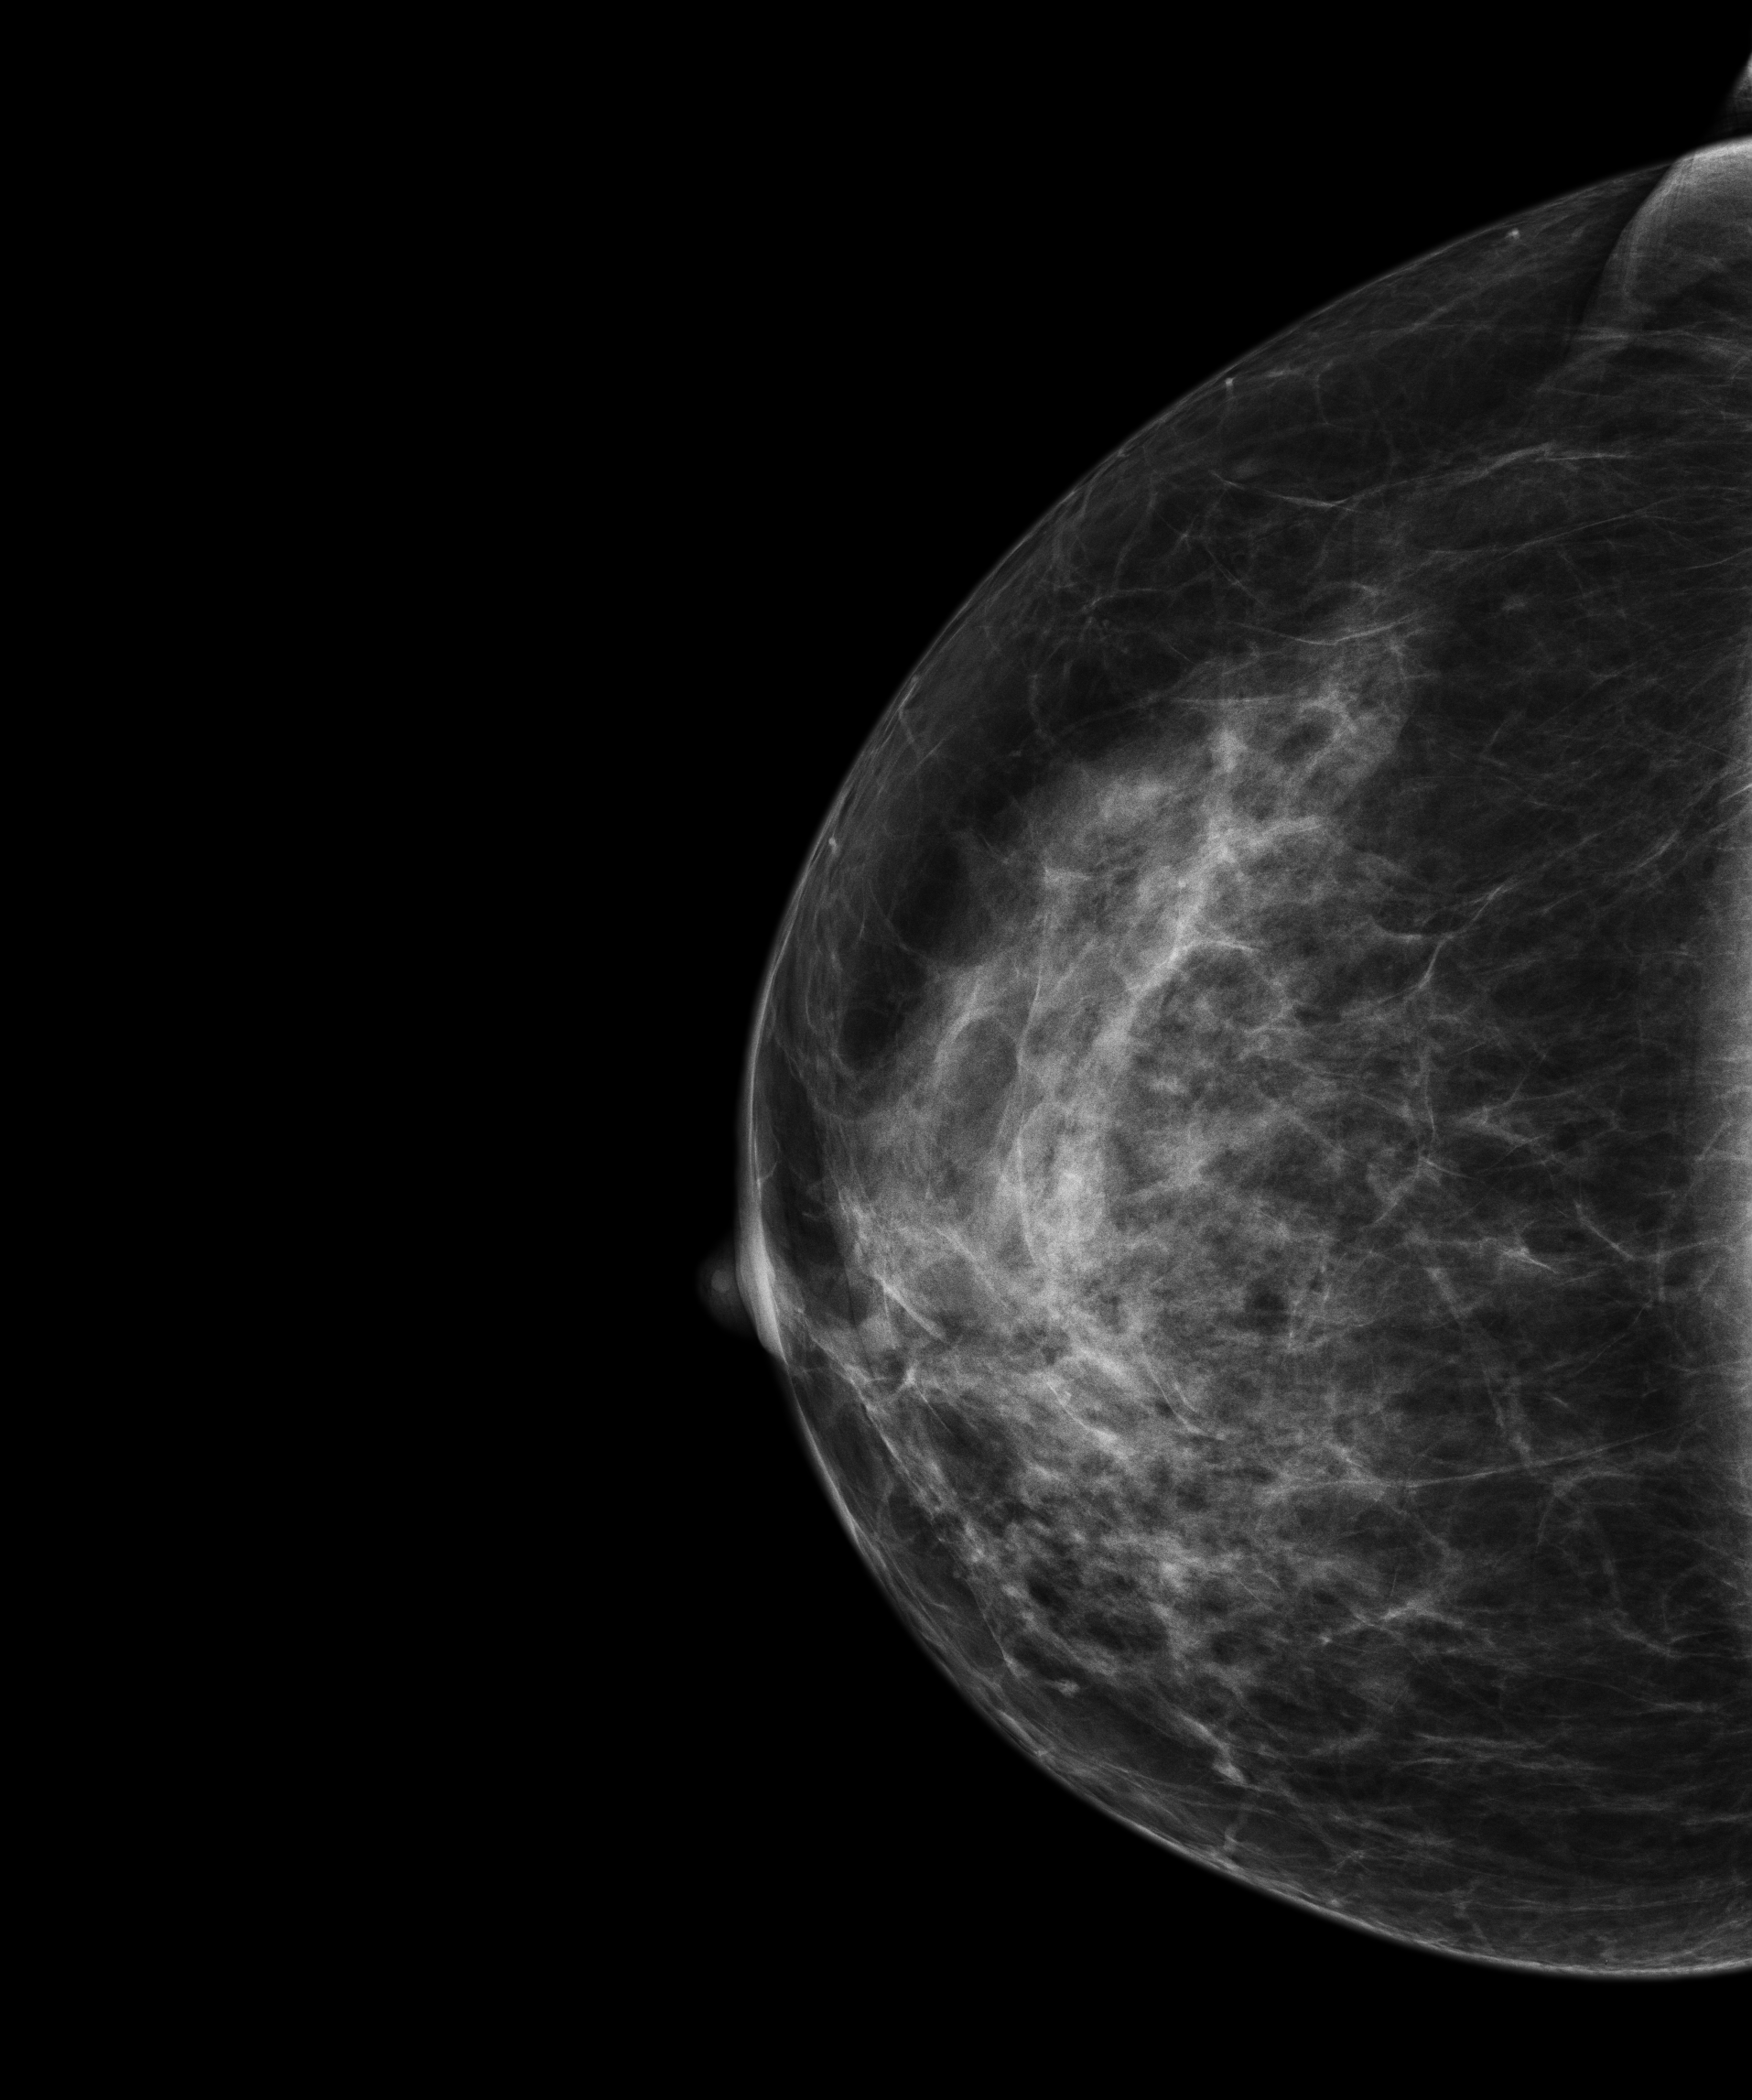
Digital mammogram (FFDM); right breast; cranio-caudal projection; annual screening mammography examination; compressed breast thickness 41 mm. Female patient, age 53 years.
BI-RADS breast density category at the screening exam (both breasts, scale 1–4): 3. Final BI-RADS assessment for this screening round (tomosynthesis exam, both breasts): category 1. Recall: no recall after this screen.